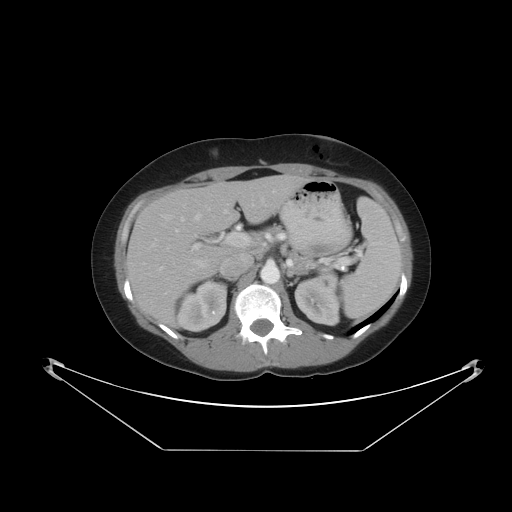
Contrast-enhanced abdominal CT, one axial slice. Slice 27 of 48 in the series (ordered by position). Reconstruction kernel STANDARD. 120 kVp. Intravenous contrast given. Soft-tissue window (W 400 / L 40 HU). 512 × 512 image matrix, field of view 482 × 482 mm. Female patient, age 38 years. From the clinical record (not read from this slice): diagnosis: colorectal cancer liver metastases, imaged before liver resection; multiple liver metastases: yes.
Structures marked on this image (manually delineated by an expert):
- hepatic veins: bounding box (x1, y1, x2, y2) in pixels: (195, 214, 201, 220)
- liver: (127, 176, 303, 325)
- planned liver remnant (the part of the liver to remain after resection): (161, 176, 303, 235)
- portal vein (with intrahepatic branches): (175, 190, 276, 268)